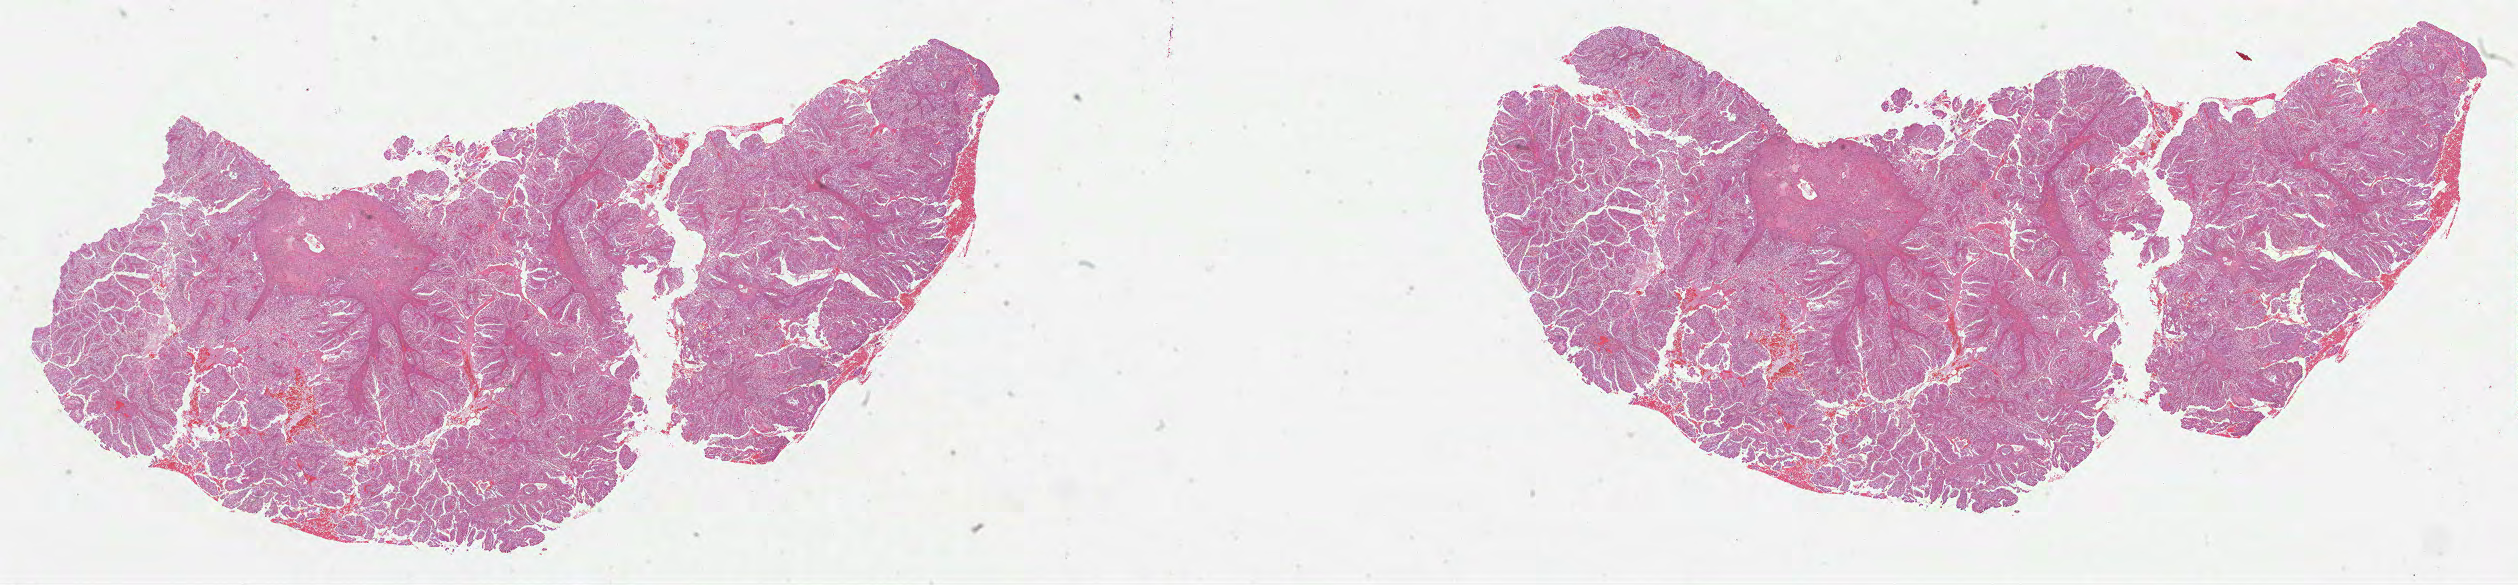
H&E whole-slide image — whole scanned area (about 40.6 x 9.4 mm, from a 40x scan) shown as a low-resolution overview. FFPE section. Sample: primary tumour, lung. Female patient; age at initial diagnosis 61 years.
- diagnosis: Adenocarcinoma, NOS (lower lobe, lung)
- AJCC pathologic stage: IB